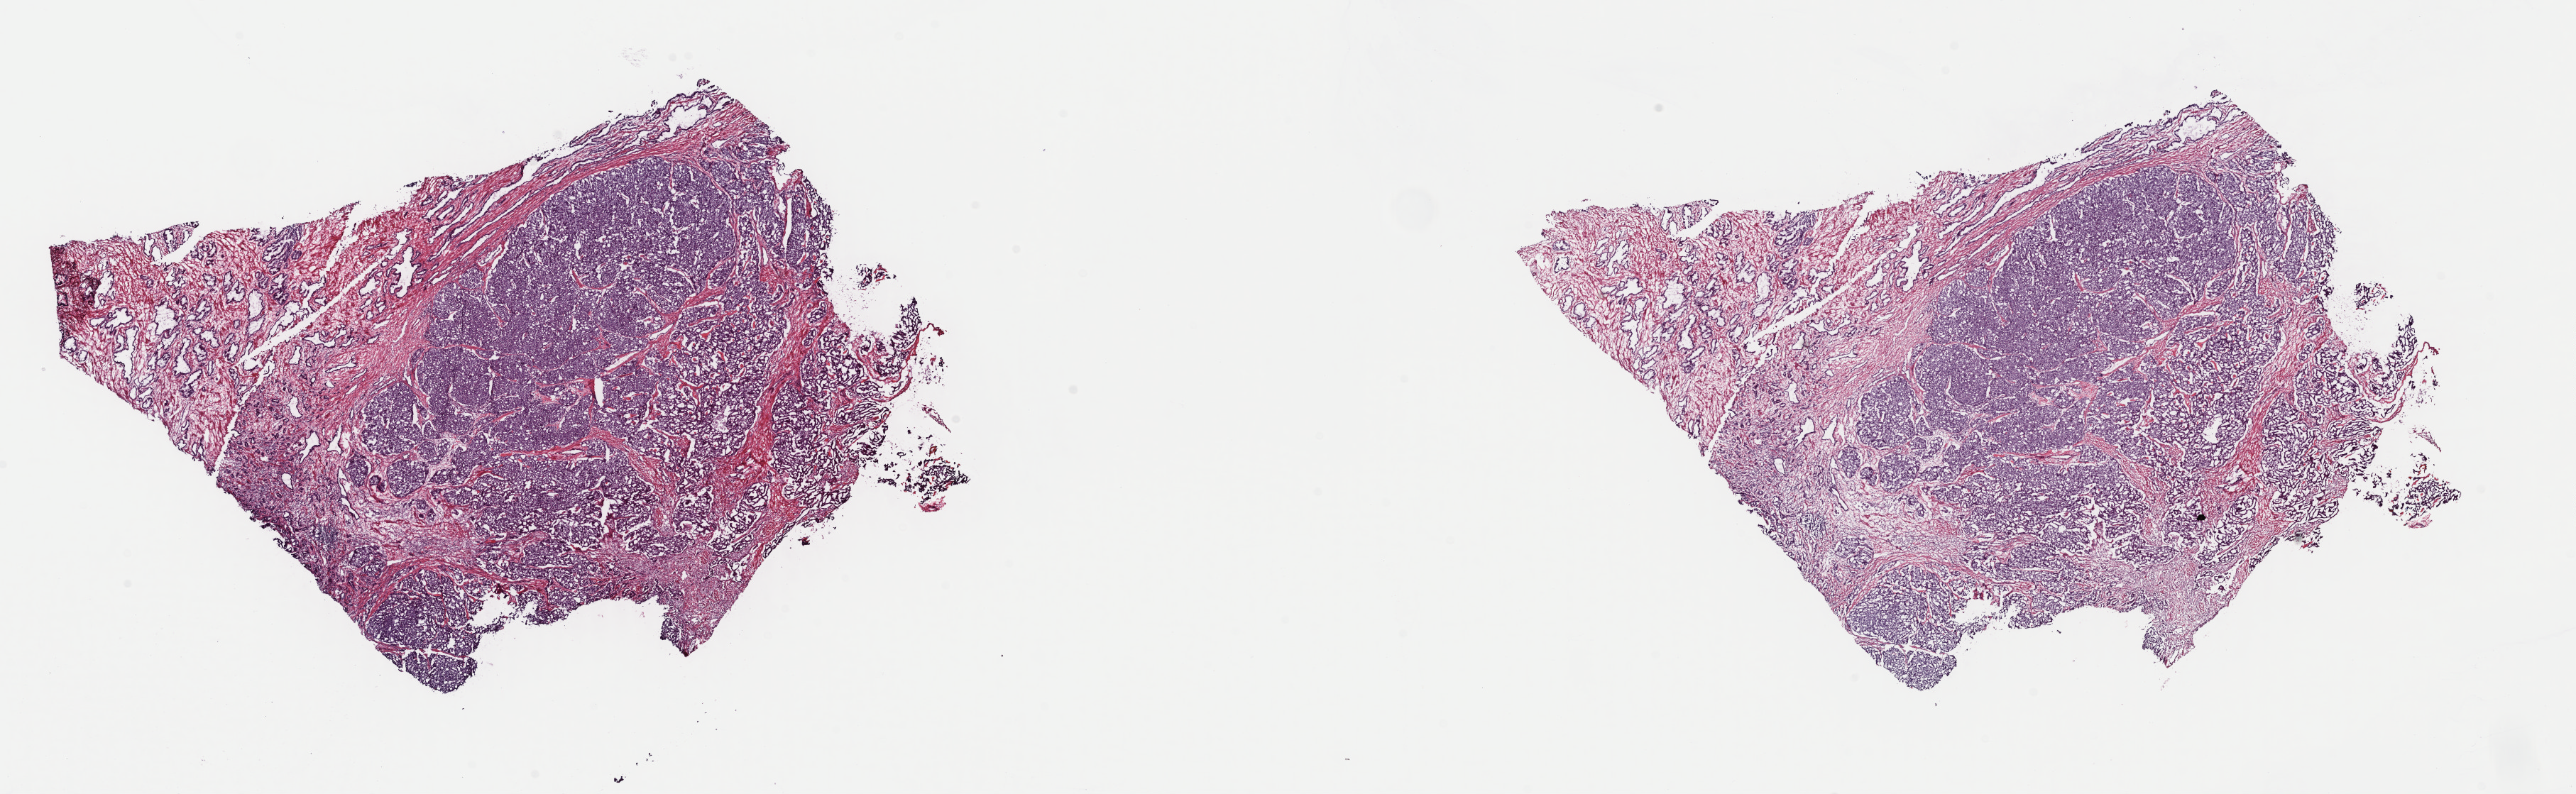
Hematoxylin and eosin (H&E) stained whole-slide image, whole scanned area (about 28.6 x 8.8 mm) shown as a low-resolution overview, frozen section from the top of the tissue portion, primary tumour sample from the prostate. Male patient; age at initial diagnosis 77 years. Gleason score: 7 (4+3). Slide review estimates, as recorded: tumour cells 70%, tumour nuclei 85%, normal cells 30%, stromal cells 0%, necrosis 0%. Inflammatory infiltration, as recorded: lymphocyte infiltration 0%, monocyte infiltration 0%, neutrophil infiltration 0%.
- lymph nodes positive (case pathology): 0 of 10 examined
- laterality: bilateral
- pathologic diagnosis: Adenocarcinoma, NOS (prostate gland)